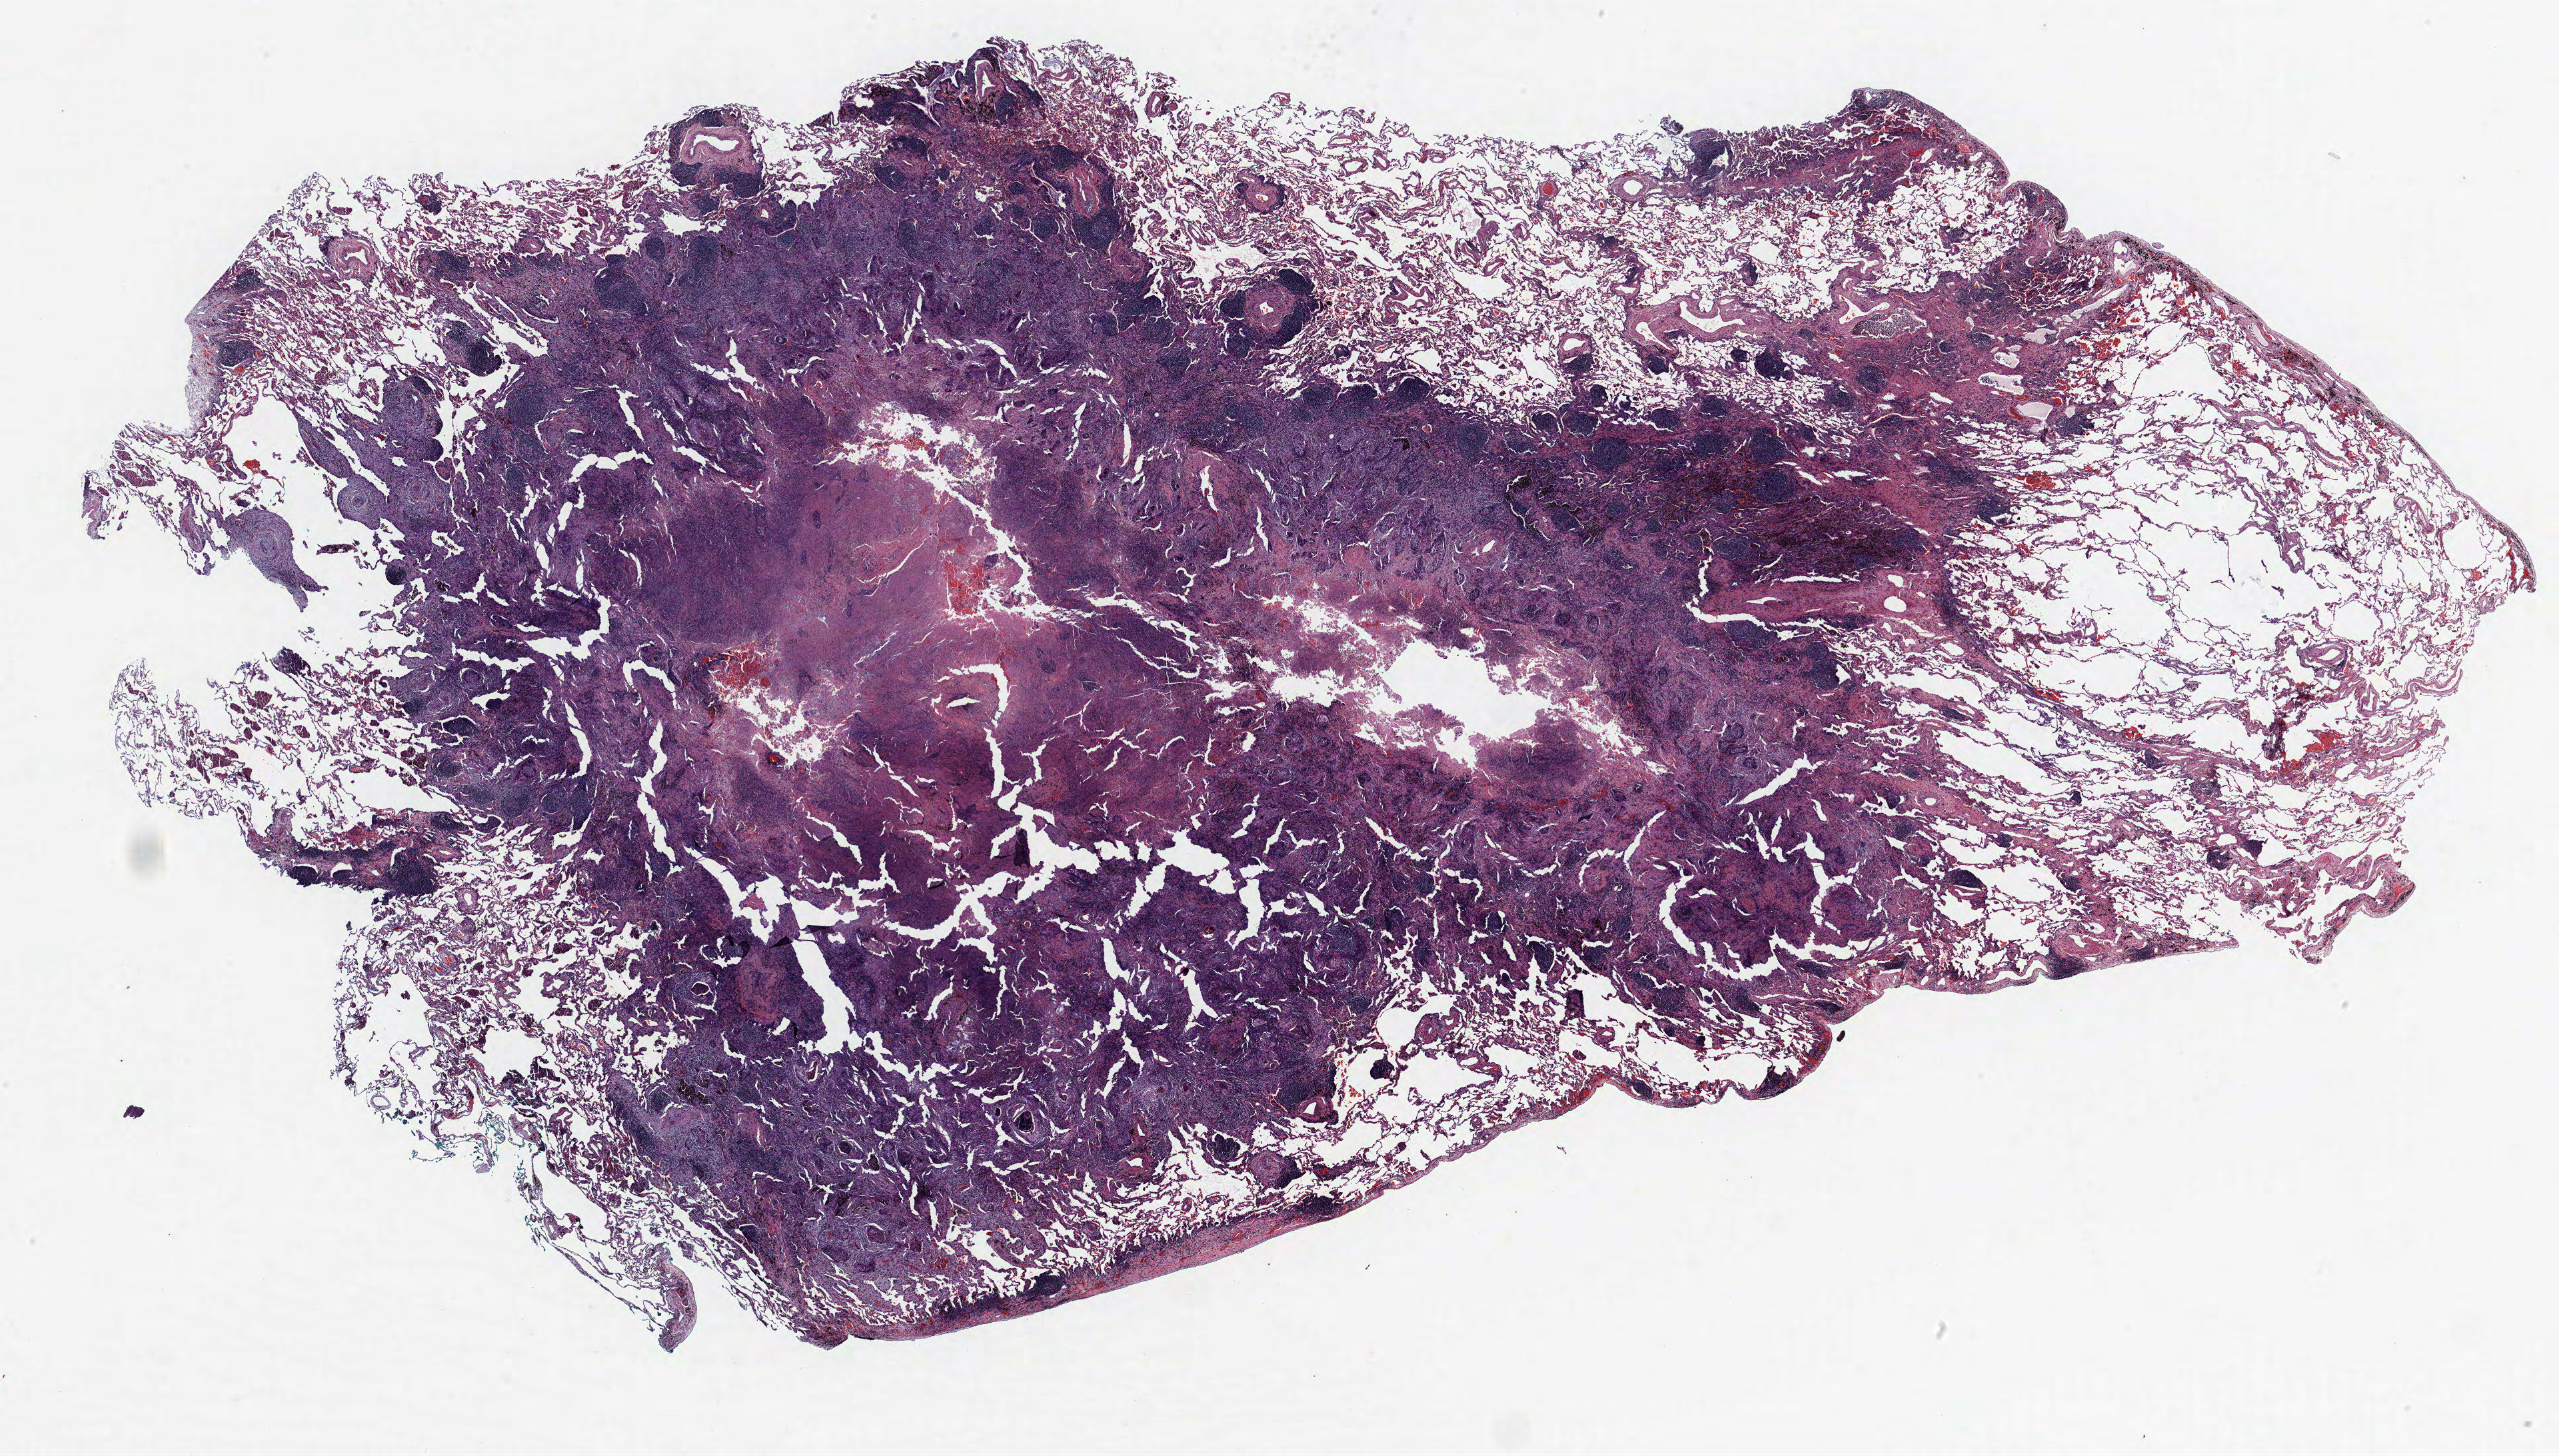
Whole-slide histology image, H&E, low-resolution overview of the scanned area, about 30.7 x 17.5 mm (from a 40x scan), formalin-fixed paraffin-embedded (FFPE) section, lung tissue. Male patient, aged 69 at enrolment. Grade: poorly differentiated (G3).
Tumour size (pathology): 15 mm. Primary tumour location (clinical record): right middle lobe. Participant's lung-cancer diagnosis: Squamous cell carcinoma, NOS. Stage (AJCC 6th edition): IA.